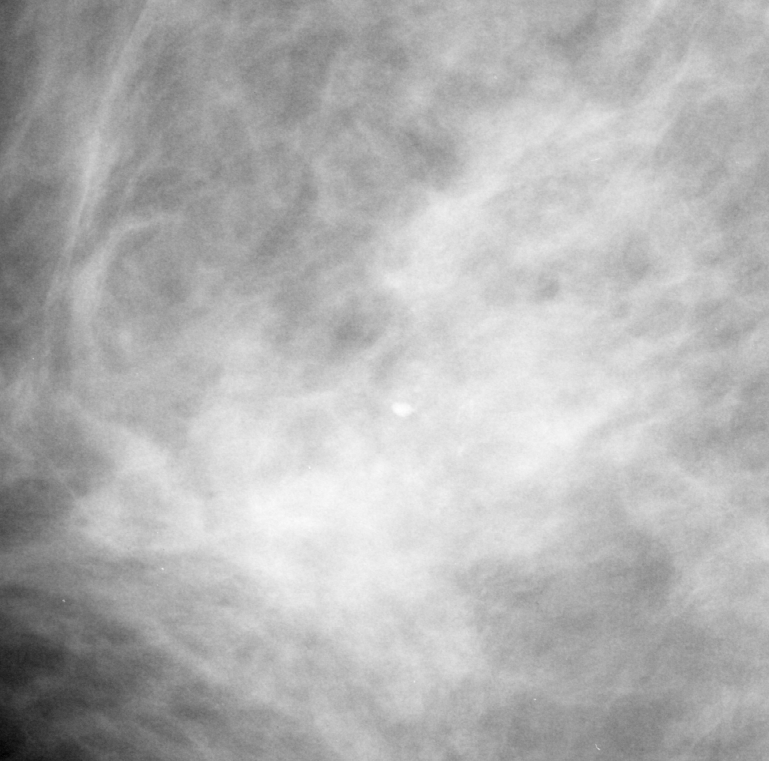
Crop from a digitized film mammogram around one marked abnormality; right breast; MLO view; BI-RADS breast density category 2 (scale 1–4).
Marked abnormality: calcifications, morphology pleomorphic, distribution clustered; BI-RADS assessment category 3; subtlety rating 2 on a 1 (subtle) to 5 (obvious) scale; pathology result (as recorded, not read from the image): malignant.